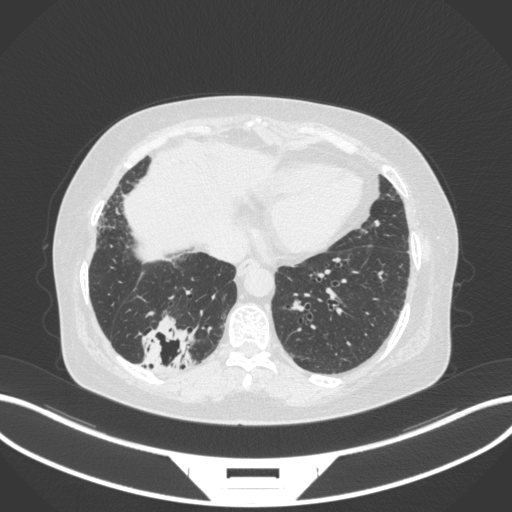
Chest CT, one axial slice; 120 kVp; lung window (W 1500 / L -600 HU); 1 mm slice thickness; 512 × 512 image matrix, field of view 400 × 400 mm. Female patient, age 65 years. From the clinical record (not read from this slice): clinical TNM (as recorded): T2b N1 M0; histopathological grade: G1.
Outlined on this slice (bounding box drawn by a radiologist):
- lung tumour (recorded histology: adenocarcinoma): bounding box (x1, y1, x2, y2) in pixels: (134, 309, 196, 372)